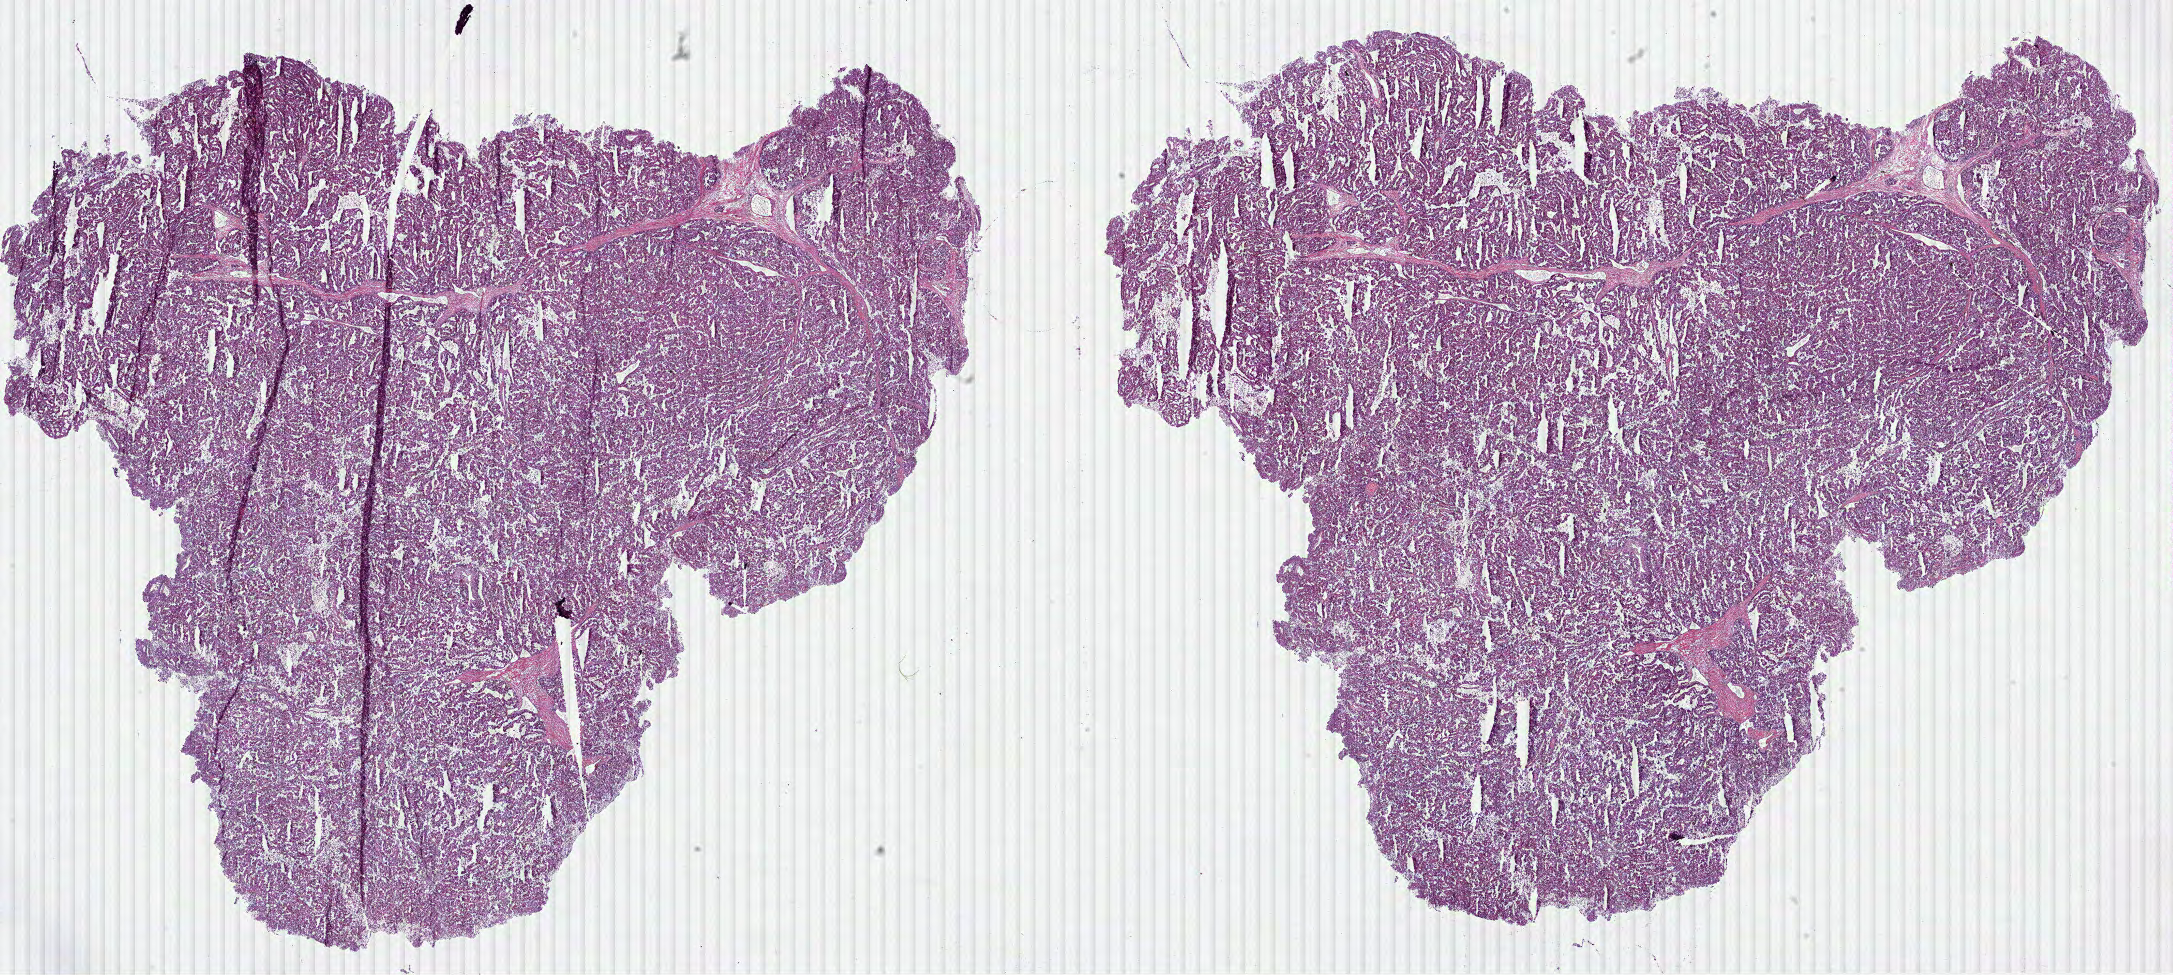
H&E whole-slide image, whole scanned area (about 35.1 x 15.7 mm) shown as a low-resolution overview; frozen section from the bottom of the tissue portion; primary tumour sample from the kidney. Female patient; age at initial diagnosis 66 years. Slide review estimates, as recorded: tumour cells 92%, tumour nuclei 85%, normal cells 0%, stromal cells 5%, necrosis 3%.
TNM: T3a NX M0. Laterality: left. Diagnosis: Papillary adenocarcinoma, NOS. AJCC pathologic stage: III.